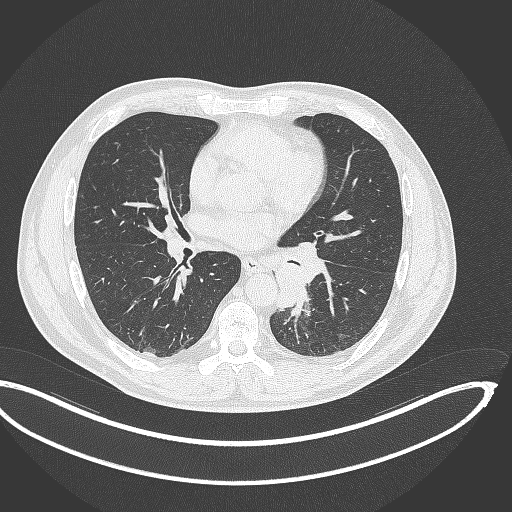
Chest CT, one axial slice. 120 kVp. Lung window (W 1500 / L -600 HU). 1 mm slice thickness. 512 × 512 image matrix. Patient: male, 50 years. From the clinical record (not read from this slice): clinical TNM (as recorded): T2a N3 M0.
Annotated regions visible in this slice (bounding box drawn by a radiologist):
- lung tumour (recorded histology: squamous cell carcinoma): bounding box (x1, y1, x2, y2) in pixels: (270, 243, 327, 312)